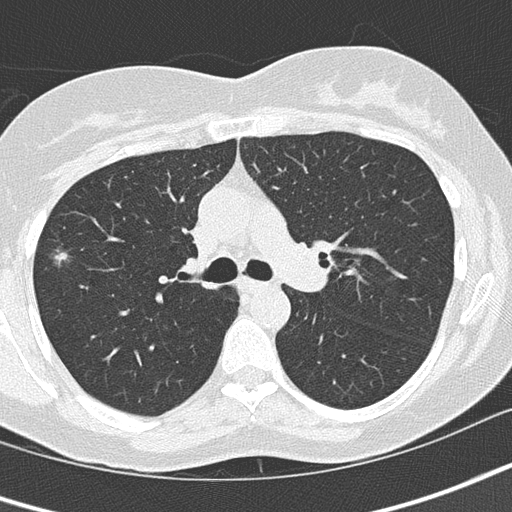
Axial slice from a low-dose chest CT screening exam, baseline screening round, lung window (W 1500 / L -600 HU), 2 mm slice thickness, lung (sharp) reconstruction kernel (B50f), slice 56 of 152 in the series, 512 × 512 image matrix. Female participant, aged 64 years at enrolment.
Expert-annotated lung lesion, box from (x=28, y=231) to (x=84, y=286) px. The screening reader recorded 4 non-calcified nodules or masses ≥4 mm on this exam (right upper lobe, left upper lobe, left upper lobe, left lower lobe); which of them this box marks is not recorded. Official screen result: positive, change unspecified: nodule(s) >= 4 mm or enlarging nodule(s), mass(es), or other non-specific abnormalities suspicious for lung cancer. Participant outcome: lung cancer diagnosed 447 days after this screen (after the second annual screen) — bronchiolo-alveolar adenocarcinoma, NOS, right upper lobe, well differentiated (G1), stage IA (AJCC 6th edition), 10 mm at pathology.